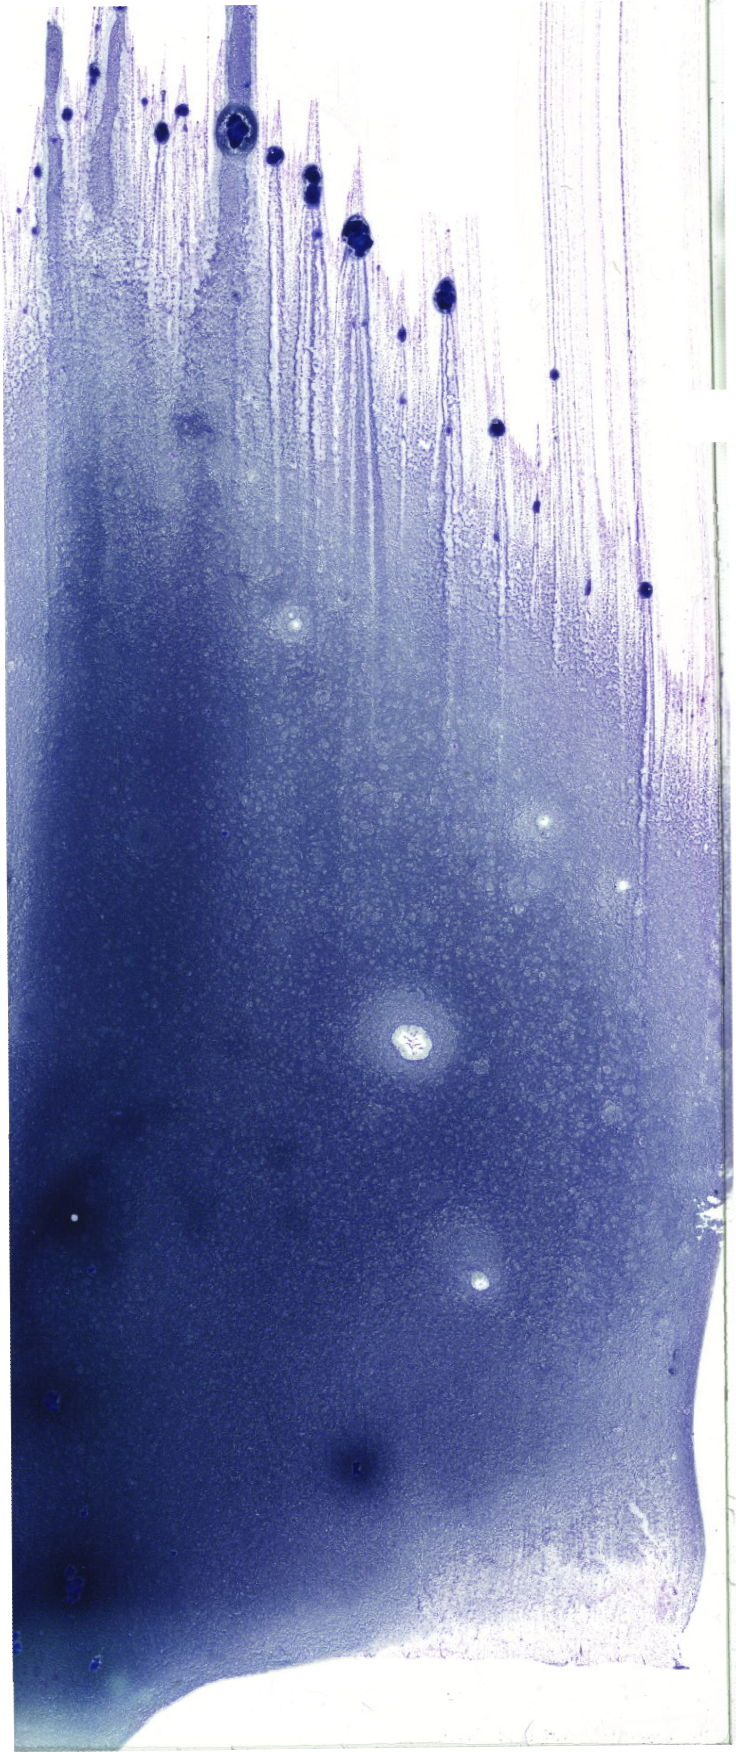
Whole-slide image of a May-Grünwald-Giemsa (MGG)-stained bone marrow aspirate smear — a low-resolution overview of the entire scanned area, about 20.9 x 49.7 mm. Patient sex: male.
Diagnosis: Mixed Phenotype Acute Leukemia, B/Myeloid.